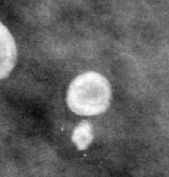
Crop from a digitized film mammogram around one marked abnormality; left breast; MLO view.
Finding: calcifications, morphology round and regular / eggshell; BI-RADS assessment category 2; subtlety rating 3 on a 1 (subtle) to 5 (obvious) scale; benign; no additional work-up was recommended (benign without callback).